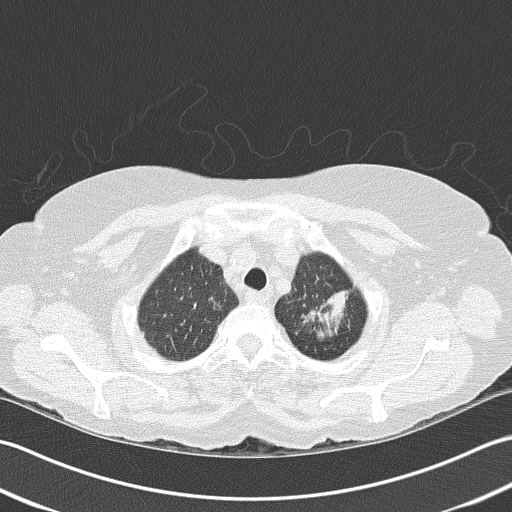
Axial slice from a low-dose chest CT screening exam; baseline annual screen; lung window (W 1500 / L -600 HU); slice 136 of 159 in the series; 512 × 512 image matrix, field of view 350 × 350 mm. Female, age 68 years at enrolment. Former smoker at enrolment.
- Expert reader's lesion annotation, box from (x=290, y=268) to (x=363, y=337) px.
- No non-calcified nodule or mass ≥4 mm was recorded by the screening reader at this exam.
- Later outcome: lung cancer diagnosed 763 days after this screen — adenocarcinoma, NOS, left upper lobe, poorly differentiated (G3), stage IB (AJCC 6th edition), 50 mm at pathology.